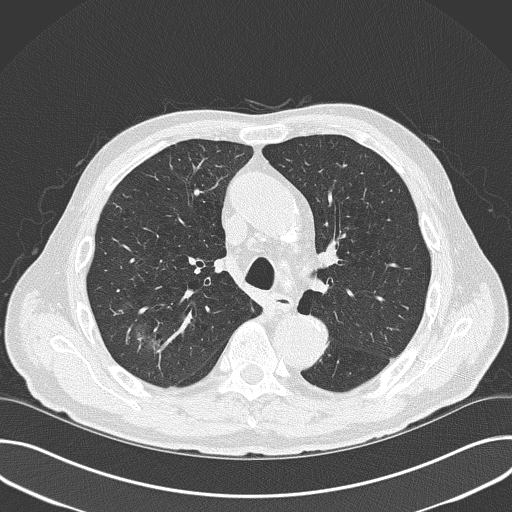
Axial slice from a low-dose chest CT screening exam. First (baseline) screen. Lung window (W 1500 / L -600 HU). 2 mm slice thickness. 120 kVp. Slice 112 of 177 in the series. 512 × 512 image matrix. Male, age 74 years at enrolment. Former smoker at enrolment.
• Expert-annotated lung lesion, box from (x=123, y=310) to (x=182, y=366) px.
• The screening reader recorded 3 non-calcified nodules or masses ≥4 mm on this exam (right upper lobe, right upper lobe, right middle lobe); which of them this box marks is not recorded.
• Official screen result: positive, change unspecified: nodule(s) >= 4 mm or enlarging nodule(s), mass(es), or other non-specific abnormalities suspicious for lung cancer.
• Lung cancer was diagnosed 215 days after this screen: small cell carcinoma, NOS, right upper lobe, stage IV (AJCC 6th edition), 15 mm at pathology.